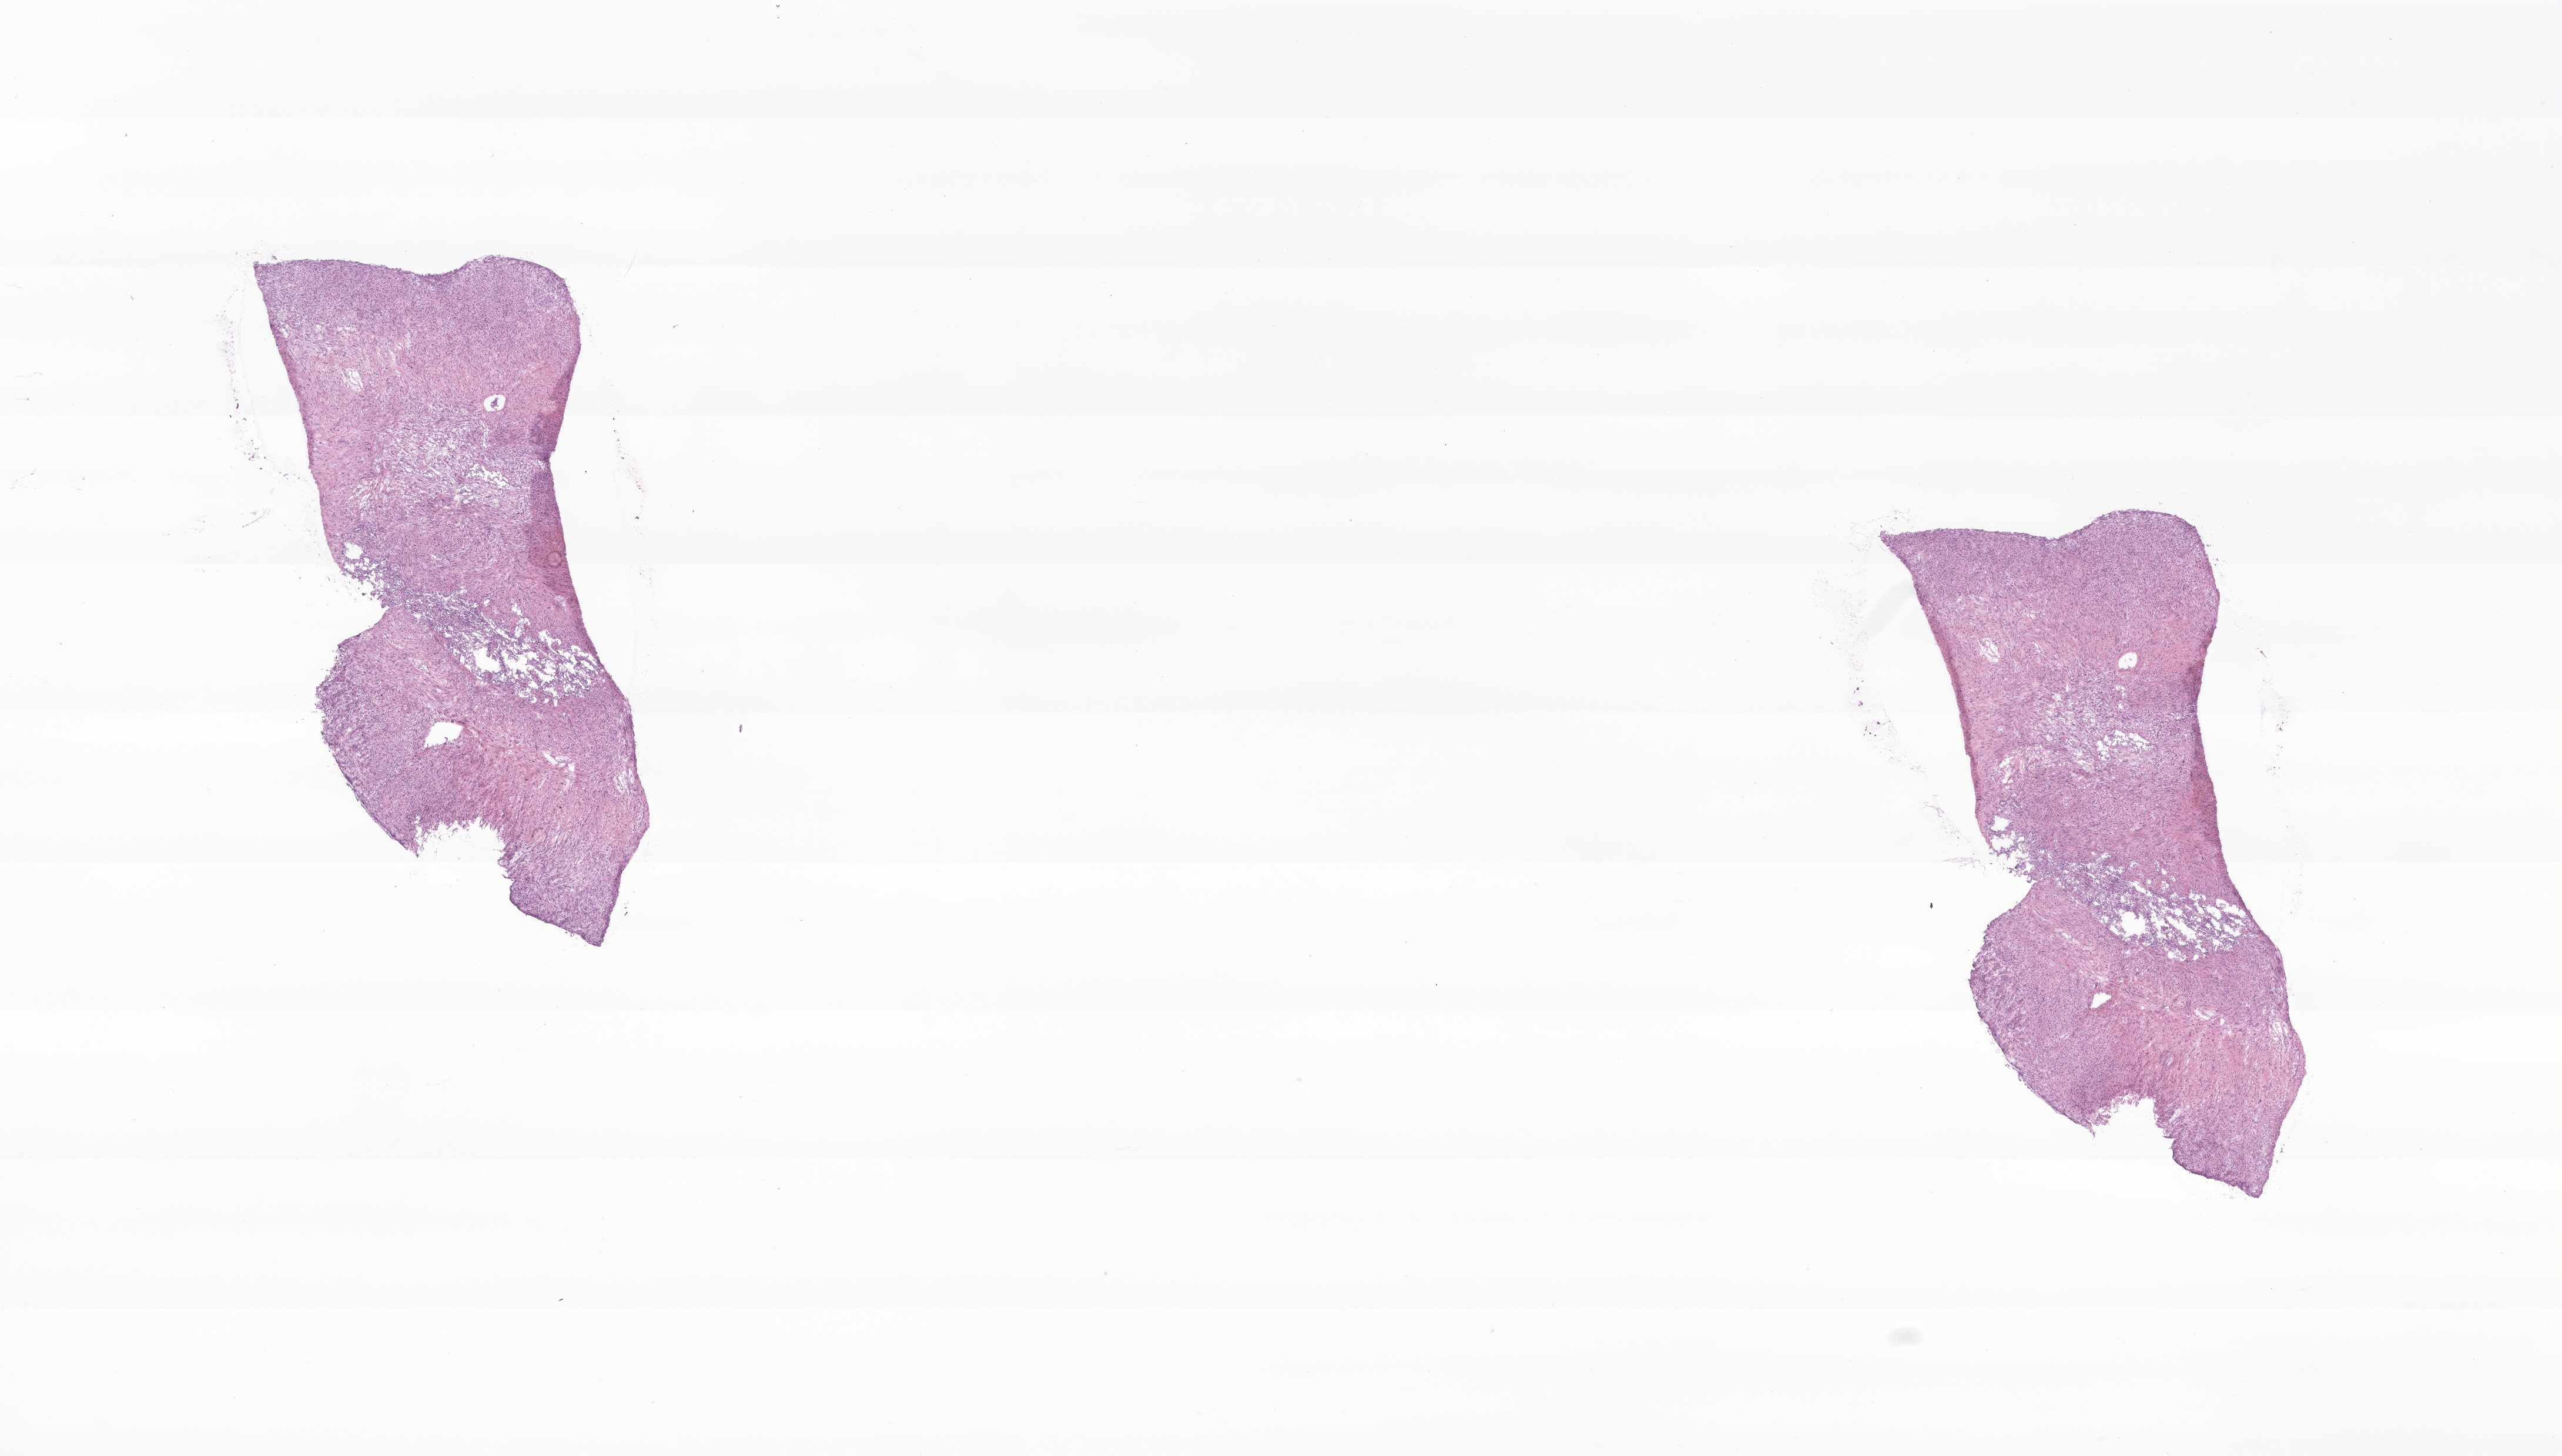
Whole-slide image, hematoxylin and eosin (H&E) stain of tumor tissue from the soft tissue of pelvis, a low-resolution overview of the entire scanned area, about 18.4 x 10.4 mm. Cryosection (OCT / tissue freezing medium). Patient female; age 190 months (15 years 10 months).
Diagnosis (ICD-O-3 morphology term): Smooth muscle tumor of uncertain malignant potential. Tissue or organ of origin (case record): connective, subcutaneous and other soft tissues of pelvis.